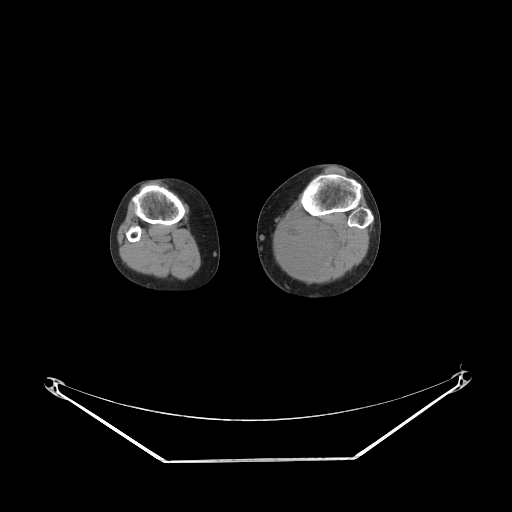
CT of an extremity soft-tissue mass (from a PET/CT study), one axial slice. Slice 156 of 223 in the series (ordered by position). 140 kVp. Soft-tissue window (W 400 / L 40 HU). 512 × 512 image matrix, field of view 500 × 500 mm. Female patient. From the clinical record (not read from this slice): histological type: extraskeletal high grade osteogenic sarcoma; grade: high; site of the primary tumour: left calf.
Structures marked on this image (expert contour drawn on MRI and transferred to this co-registered scan by the dataset authors):
- gross tumour volume (mass): box from (x=276, y=224) to (x=339, y=273) px